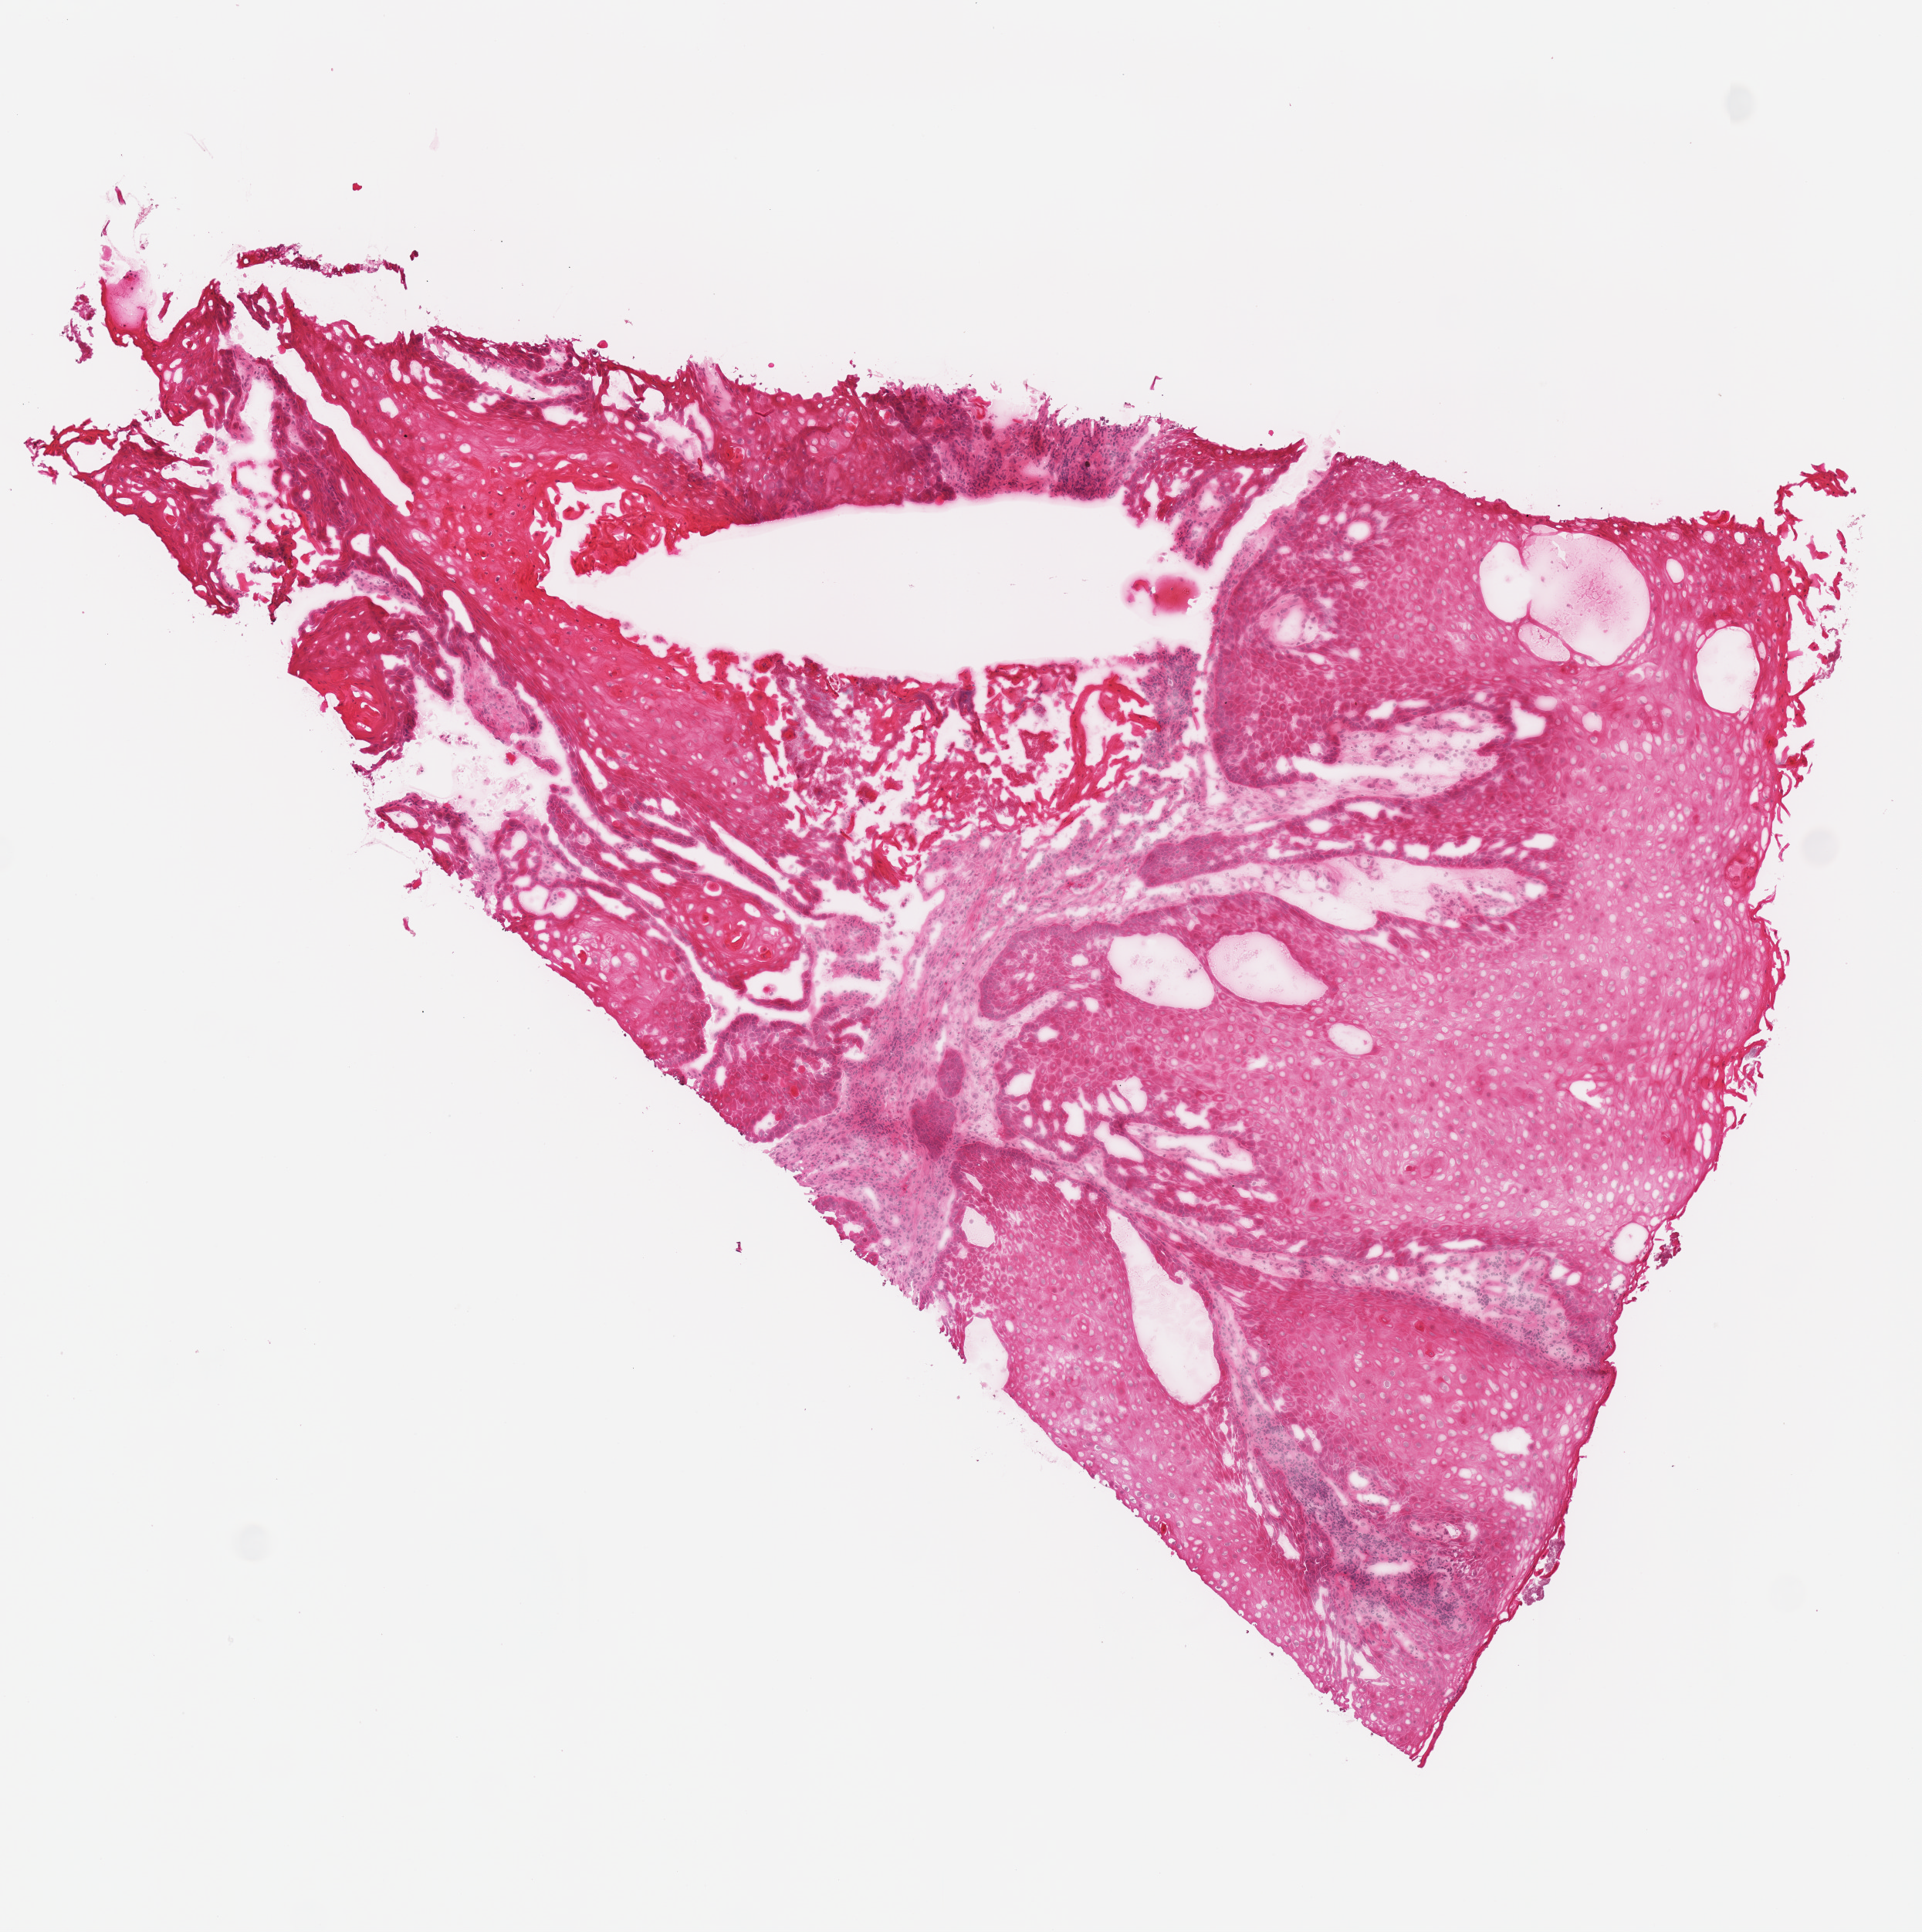
Hematoxylin and eosin (H&E) stained whole-slide image, shown as a low-resolution overview of the whole scanned area (about 4.9 x 4.9 mm); frozen section from the top of the tissue portion; head and neck, primary tumour sample. Female patient; age at initial diagnosis 43 years. Histologic grade: G2 (moderately differentiated). Composition of this section per pathologist review: tumour cells 95%, tumour nuclei 85%, normal cells 0%, stromal cells 5%, necrosis 0%.
AJCC pathologic stage: III (7th edition). TNM: T3 N0. Diagnosis: Squamous cell carcinoma, NOS (tongue, NOS).